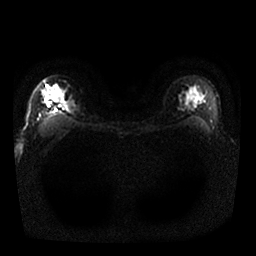
Breast MRI, one axial slice; position 19 of 25 along the scan axis; diffusion-weighted series; image 2 of 4 stored at this slice position (different b-values; order by instance number); 1.5 T; 4 mm slice thickness; 256 × 256 image matrix. Female patient.
Annotated regions visible in this slice (manually delineated by an expert):
- tumour on diffusion-weighted imaging: bounding box [x1, y1, x2, y2] px = [46, 95, 54, 100]